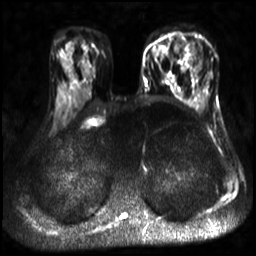
Breast MRI, one axial slice; diffusion-weighted series; image 2 of 4 stored at this slice position (different b-values; order by instance number); 3 T; 256 × 256 image matrix. Female patient.
Structures marked on this image (outlined manually by an expert reader):
- tumour on diffusion-weighted imaging: bounding box <181,40,195,54> (left, top, right, bottom; pixels)